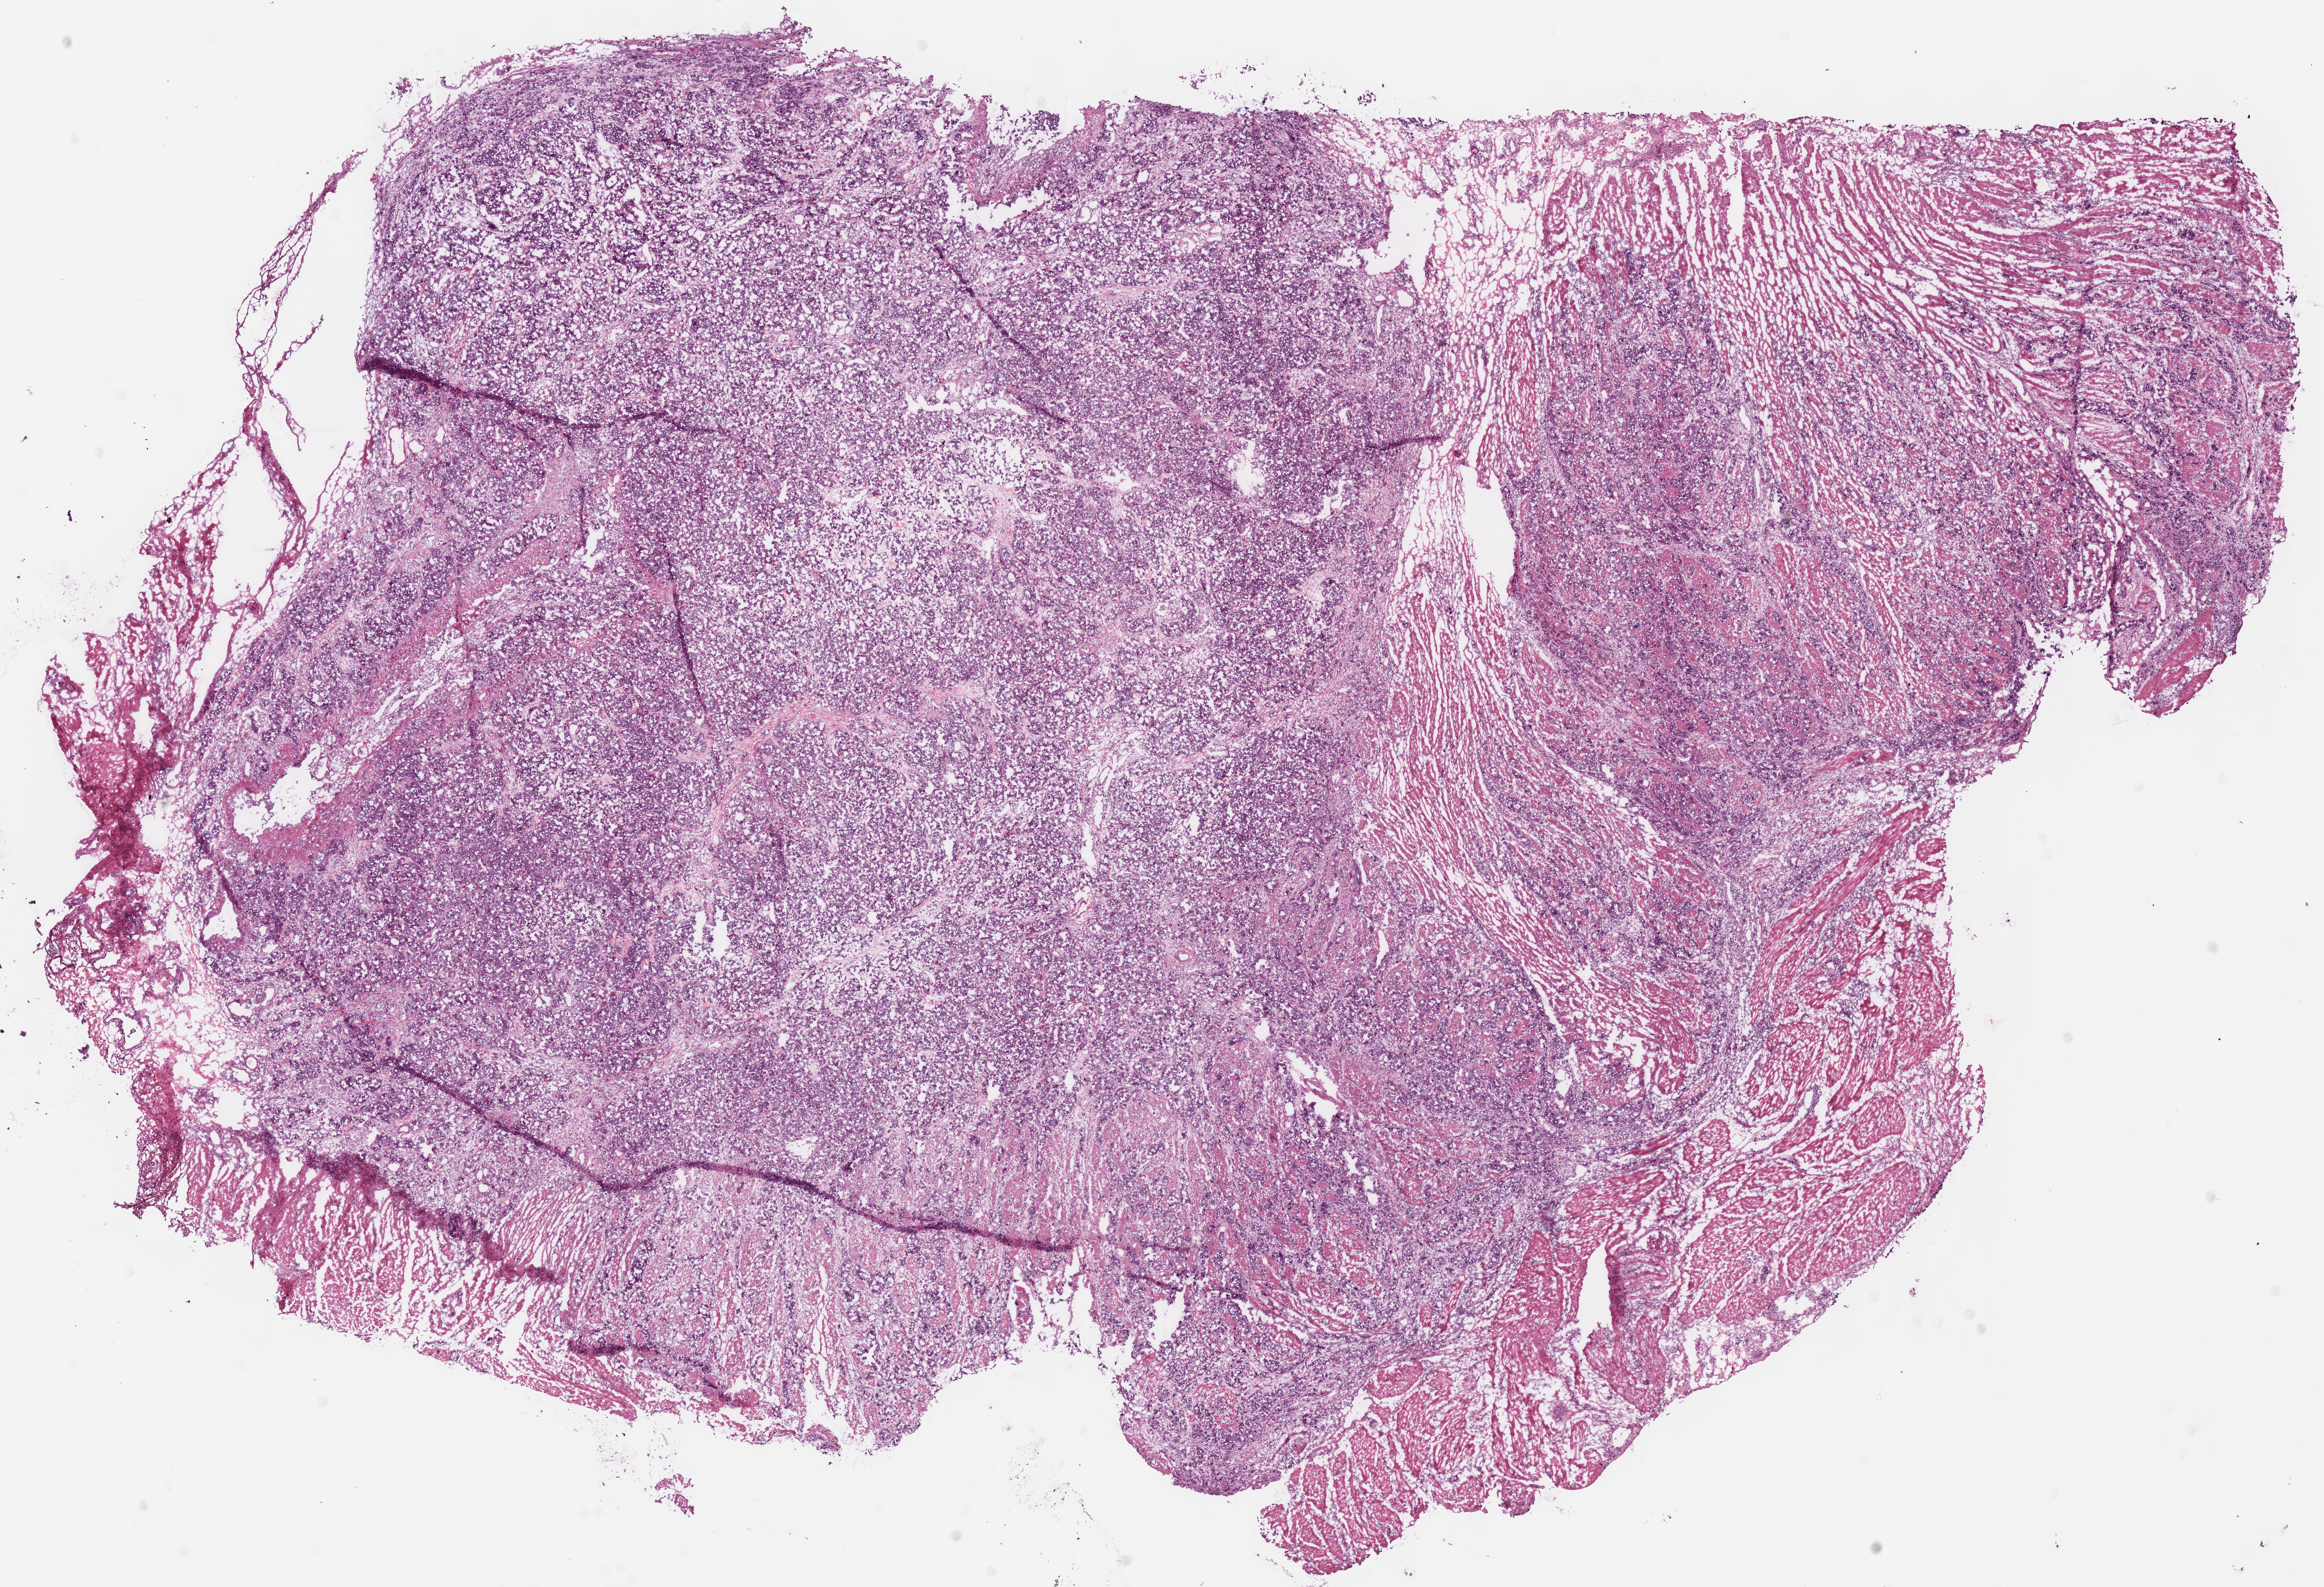
Whole-slide histology image, H&E — whole scanned area (about 15.7 x 10.7 mm, slide scanned at 40x) shown as a low-resolution overview; frozen section from the bottom of the tissue portion; primary tumour sample from the stomach. Male, age 68 years at initial diagnosis. Histologic grade: G3 (poorly differentiated). Composition of this section per pathologist review: tumour cells 90%, tumour nuclei 85%, normal cells 0%, stromal cells 10%, necrosis 0%.
Histologic diagnosis: Adenocarcinoma, NOS (cardia, NOS). AJCC pathologic stage: IIB.